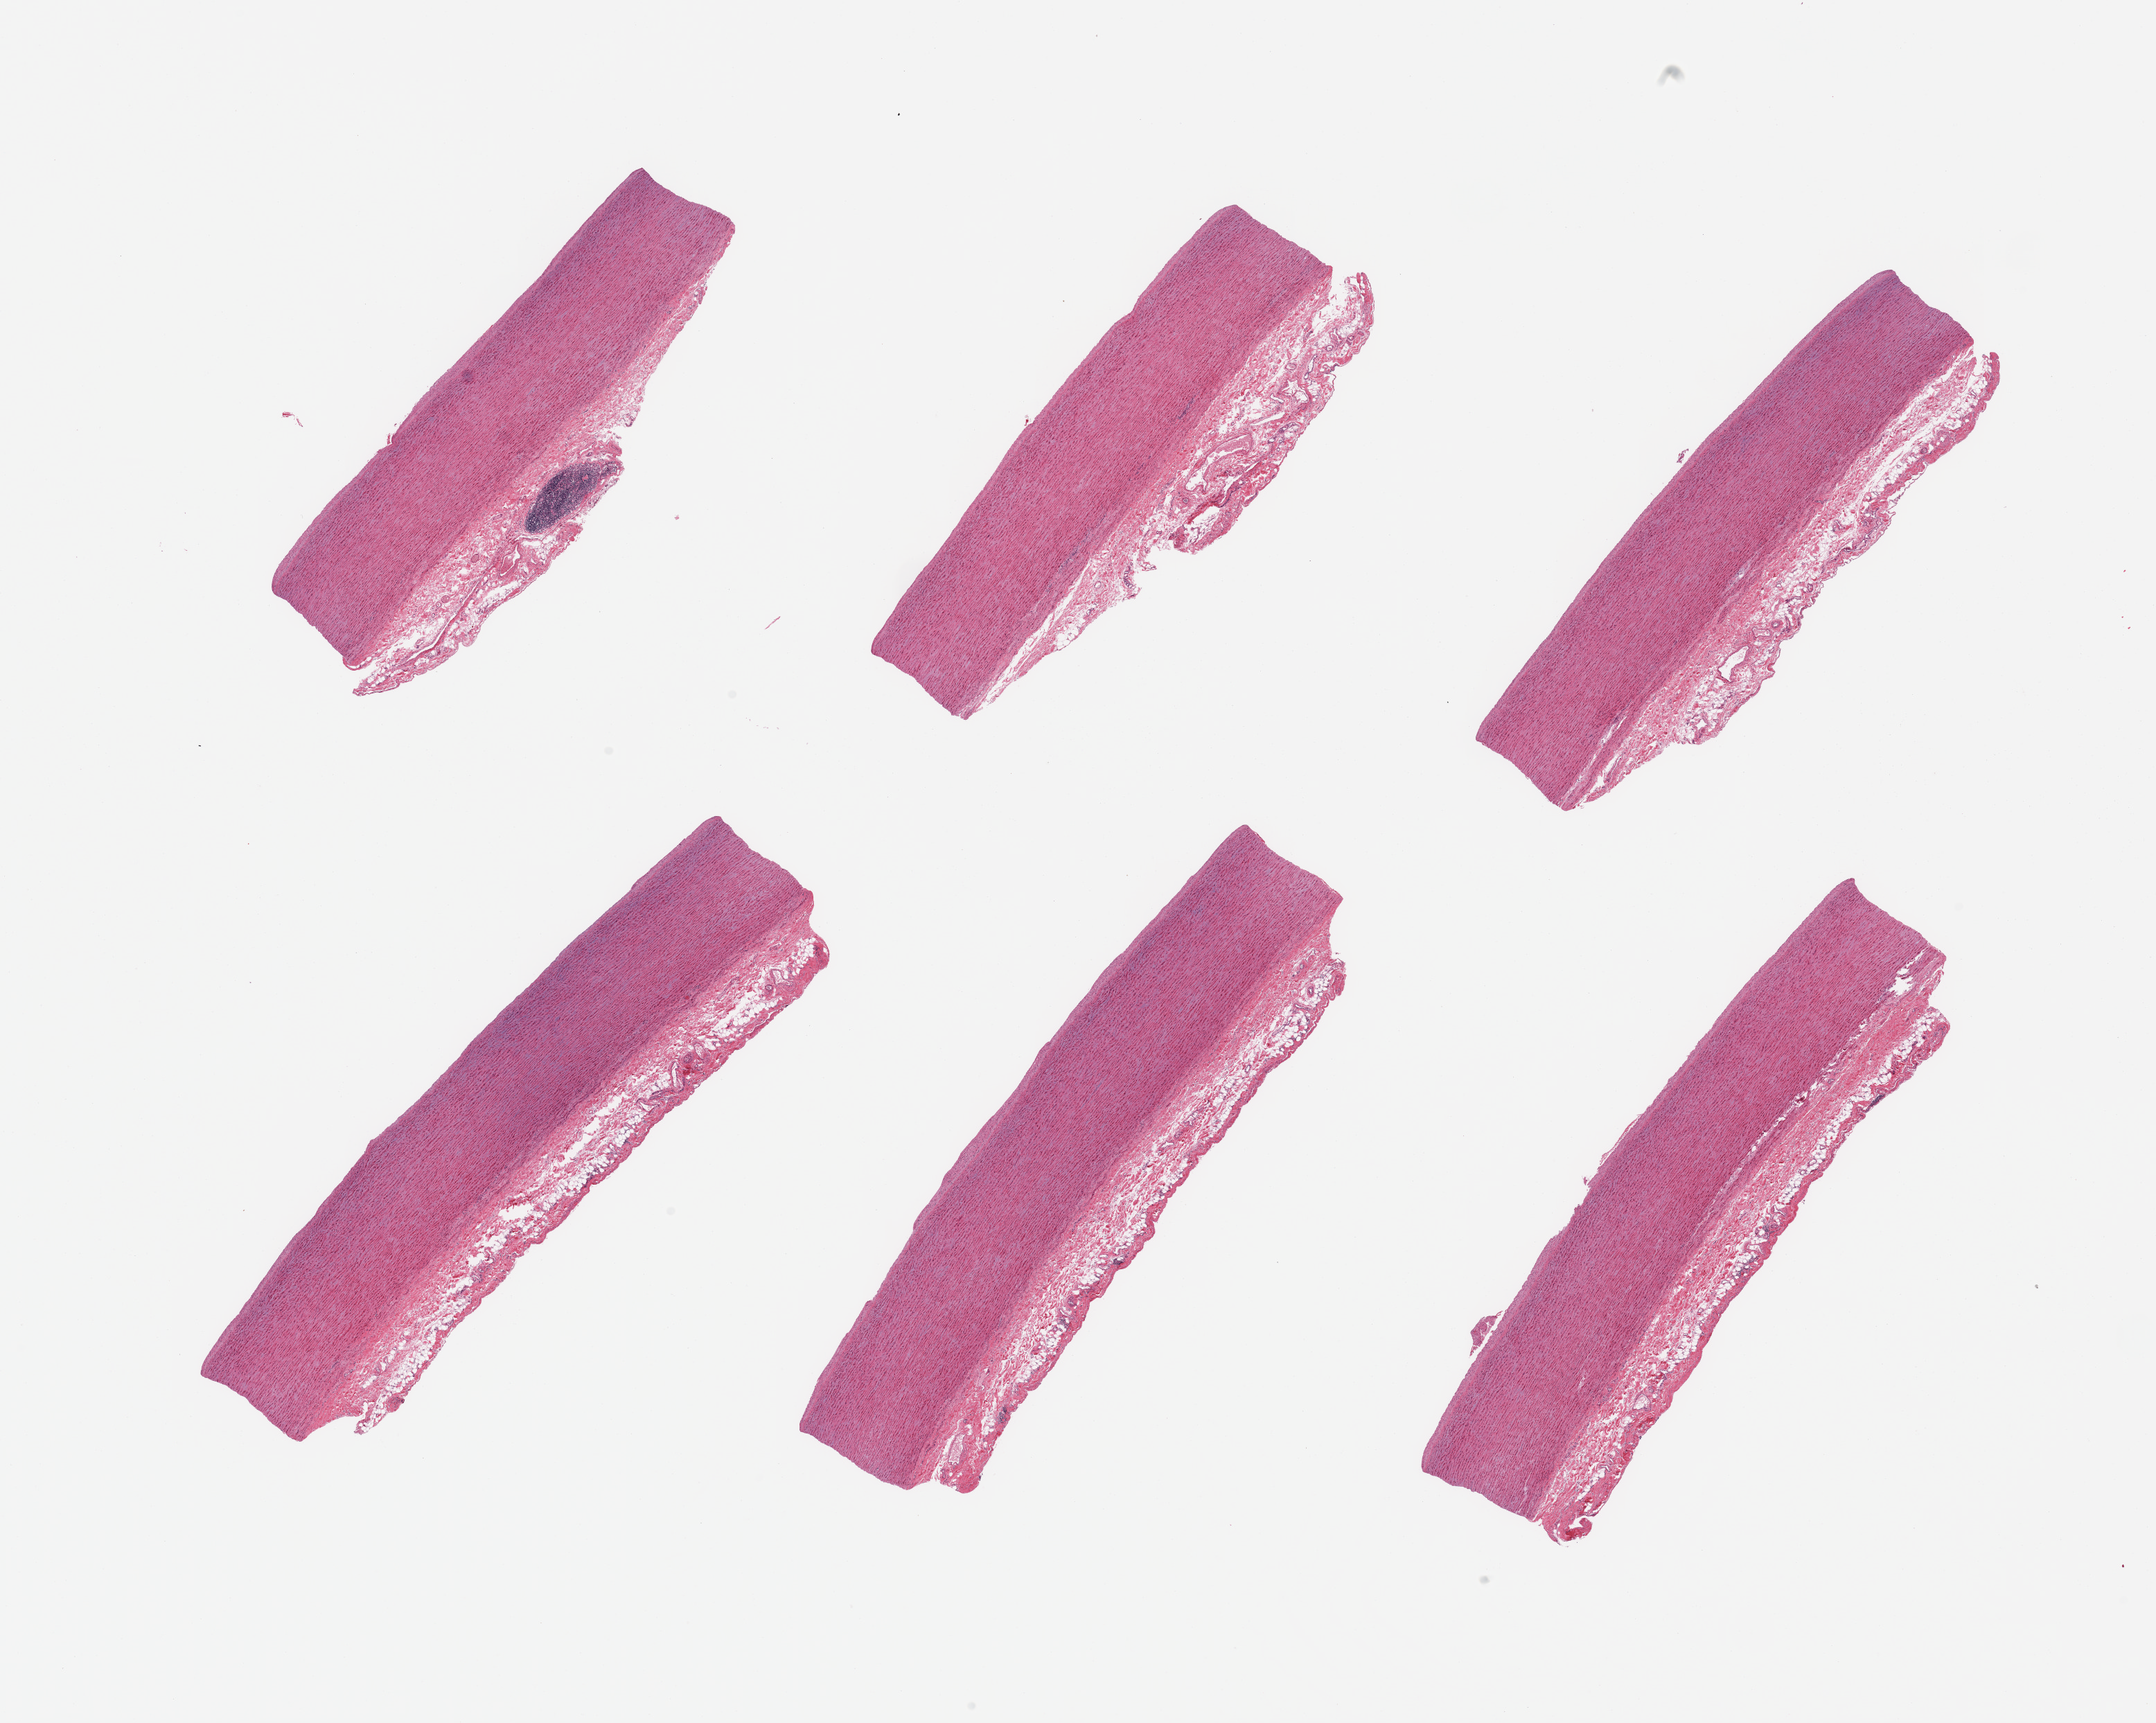
Haematoxylin and eosin whole-slide image — a low-resolution overview of the entire scanned area, about 24.6 x 19.7 mm (slide scanned at 20x). PAXgene-fixed paraffin-embedded (PFPE) section. Sampled site (target tissue): aorta. Donor tissue sample. Male donor.
Reviewer comment on this tissue sample: 6 pieces, ~minimal atherosis, ~70 microns.